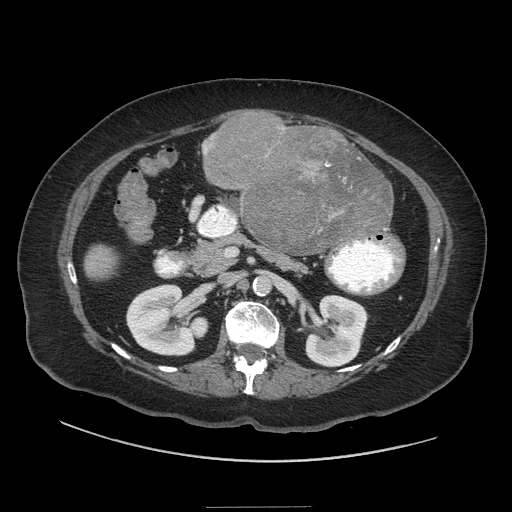
Contrast-enhanced abdominal CT (liver protocol), one axial slice; slice 6 of 81 in the series (ordered by position); 140 kVp; soft-tissue window (W 400 / L 40 HU); 512 × 512 image matrix, field of view 440 × 440 mm. Case-level facts recorded for this patient, not image findings: diagnosis: hepatocellular carcinoma (patient treated with transarterial chemoembolisation; whether this scan precedes or follows treatment is not stated here); TNM stage (as recorded): Stage-II; Child-Pugh class: A; tumour size: 1.7 cm.
Structures marked on this image (semi-automatic segmentation, software-assisted and operator-edited):
- liver parenchyma outside the tumour (the mass and vessels are separate outlines, so this box may not span the whole liver): bounding box (x1, y1, x2, y2) in pixels: (84, 128, 394, 280)
- mass: (204, 114, 390, 252)